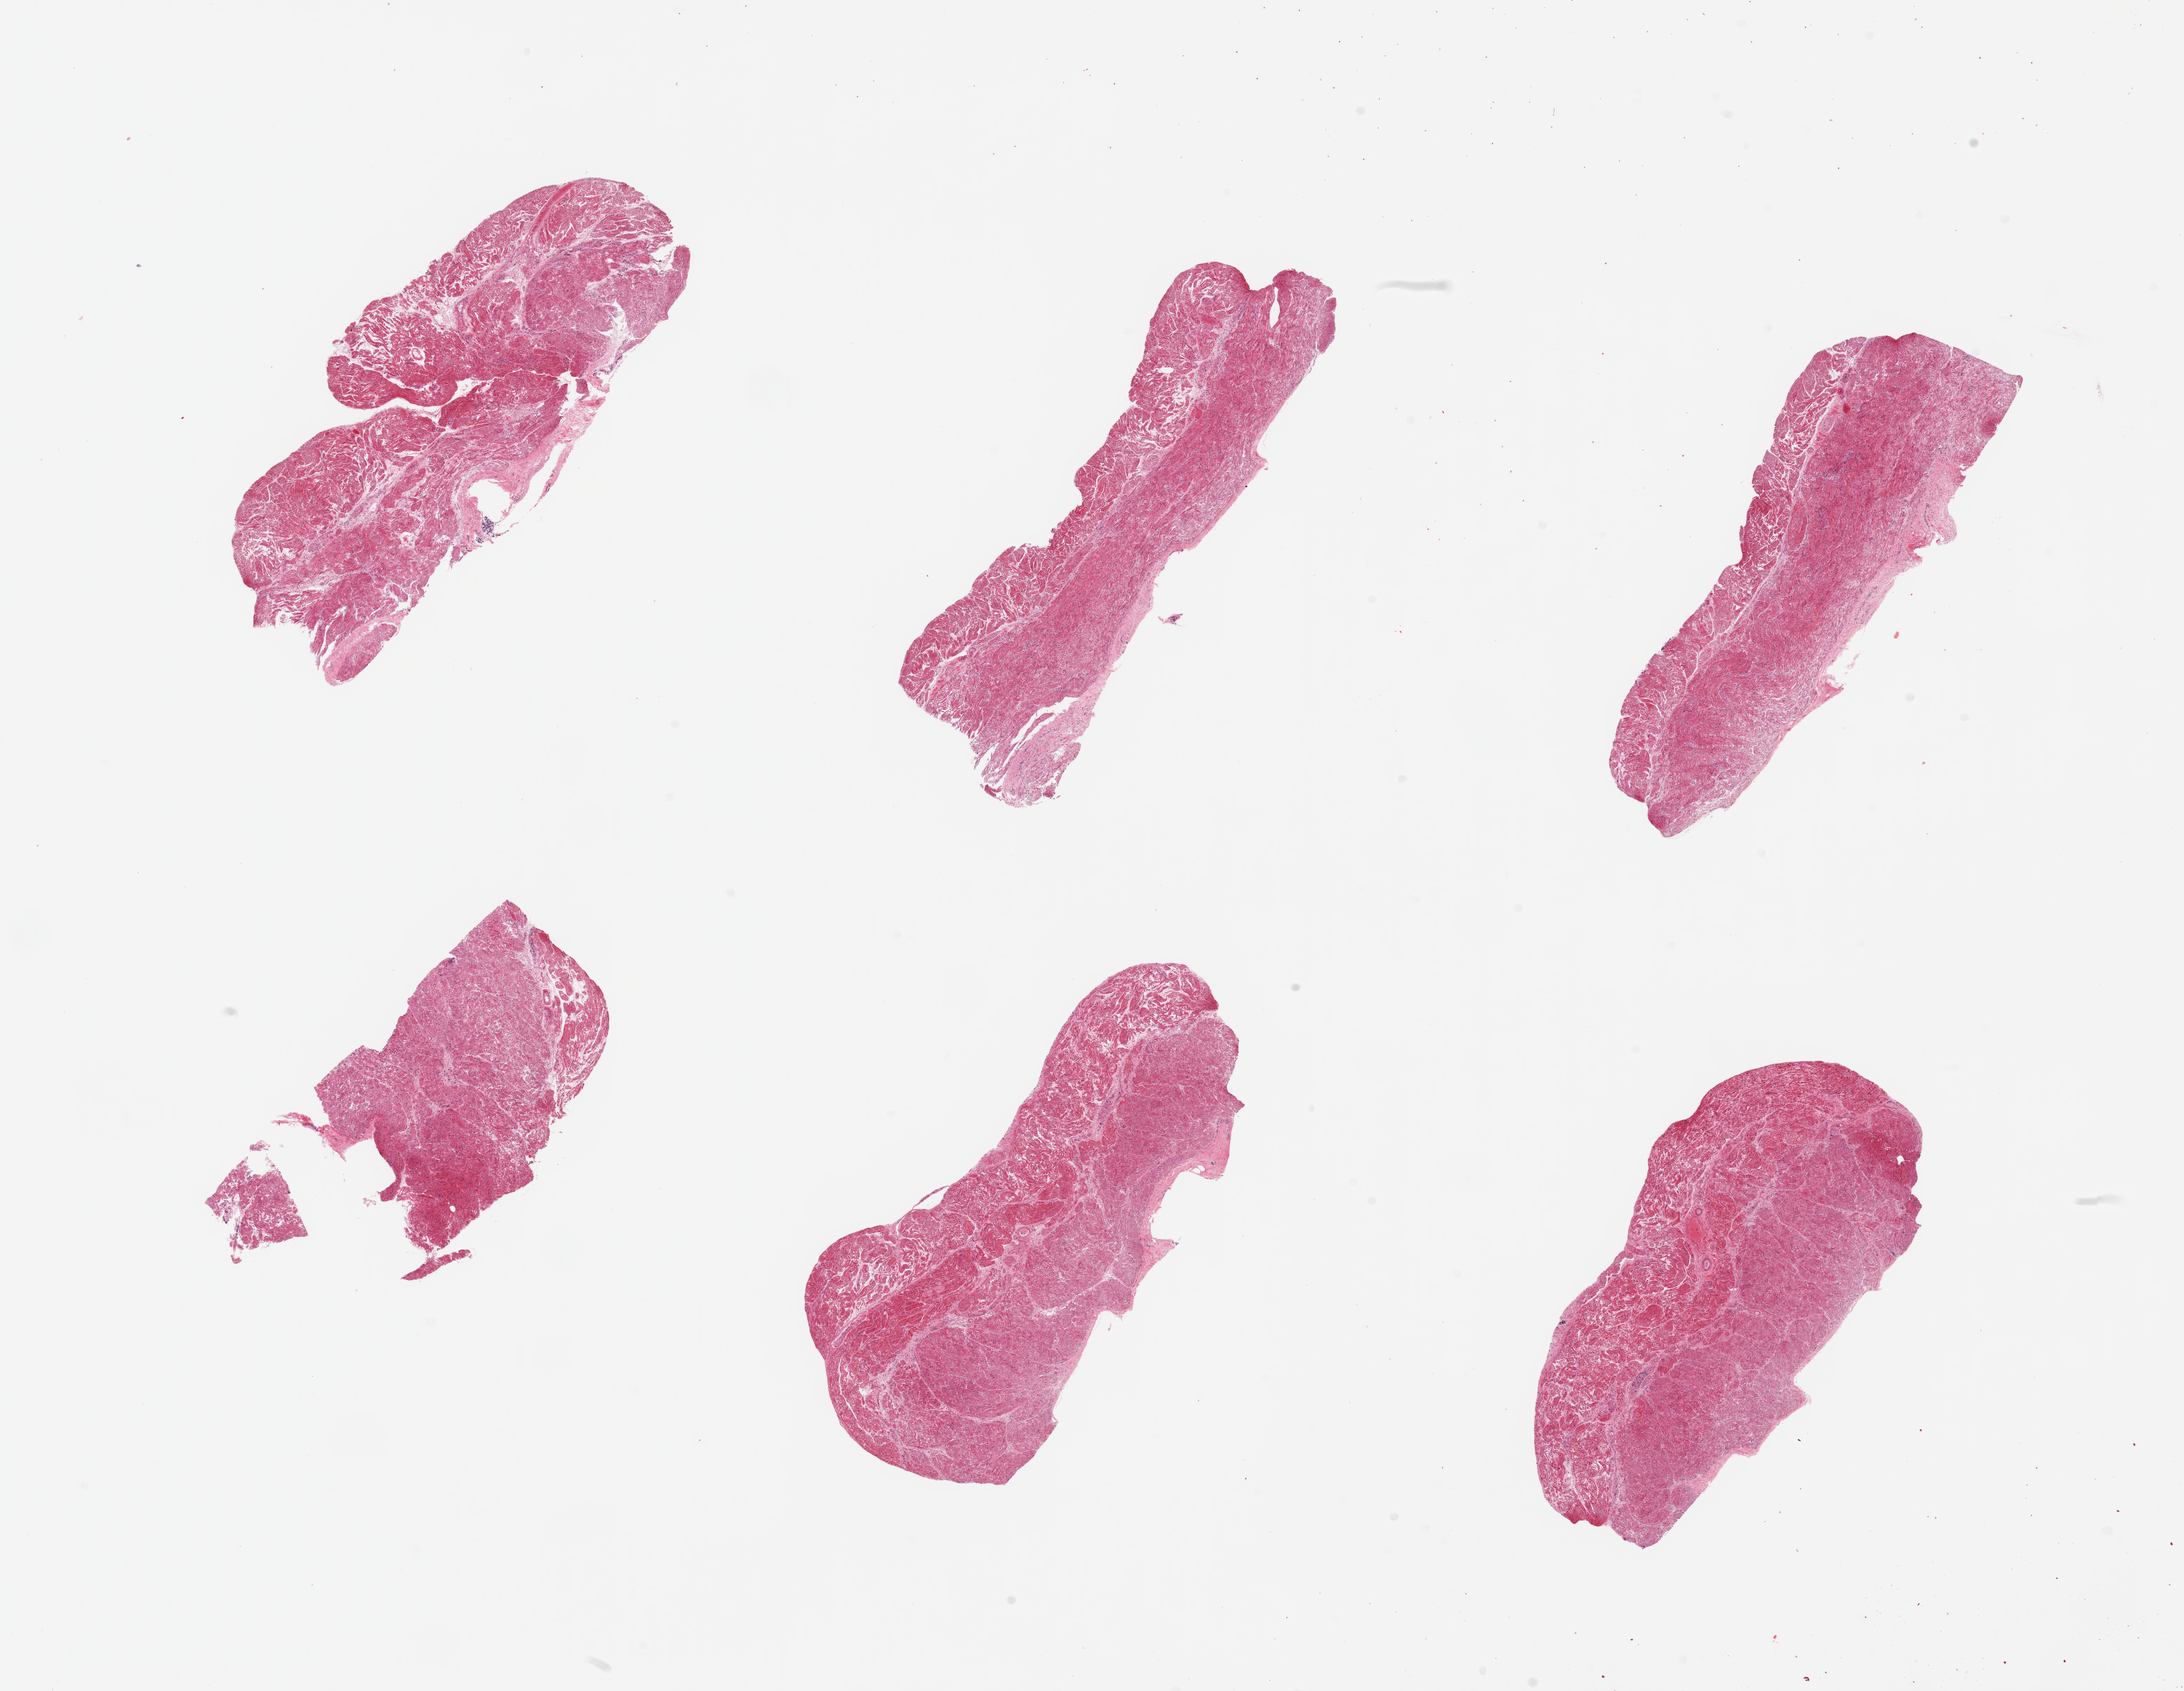
Digitized hematoxylin and eosin (H&E)-stained section, brightfield, low-resolution overview of the scanned area, about 24.6 x 19.1 mm (acquisition: 20x scan), PAXgene-fixed, paraffin-embedded tissue, target tissue: esophageal muscle, tissue donor sample. Male donor.
Review note (as recorded): 6 pieces, confirmed target muscularis.